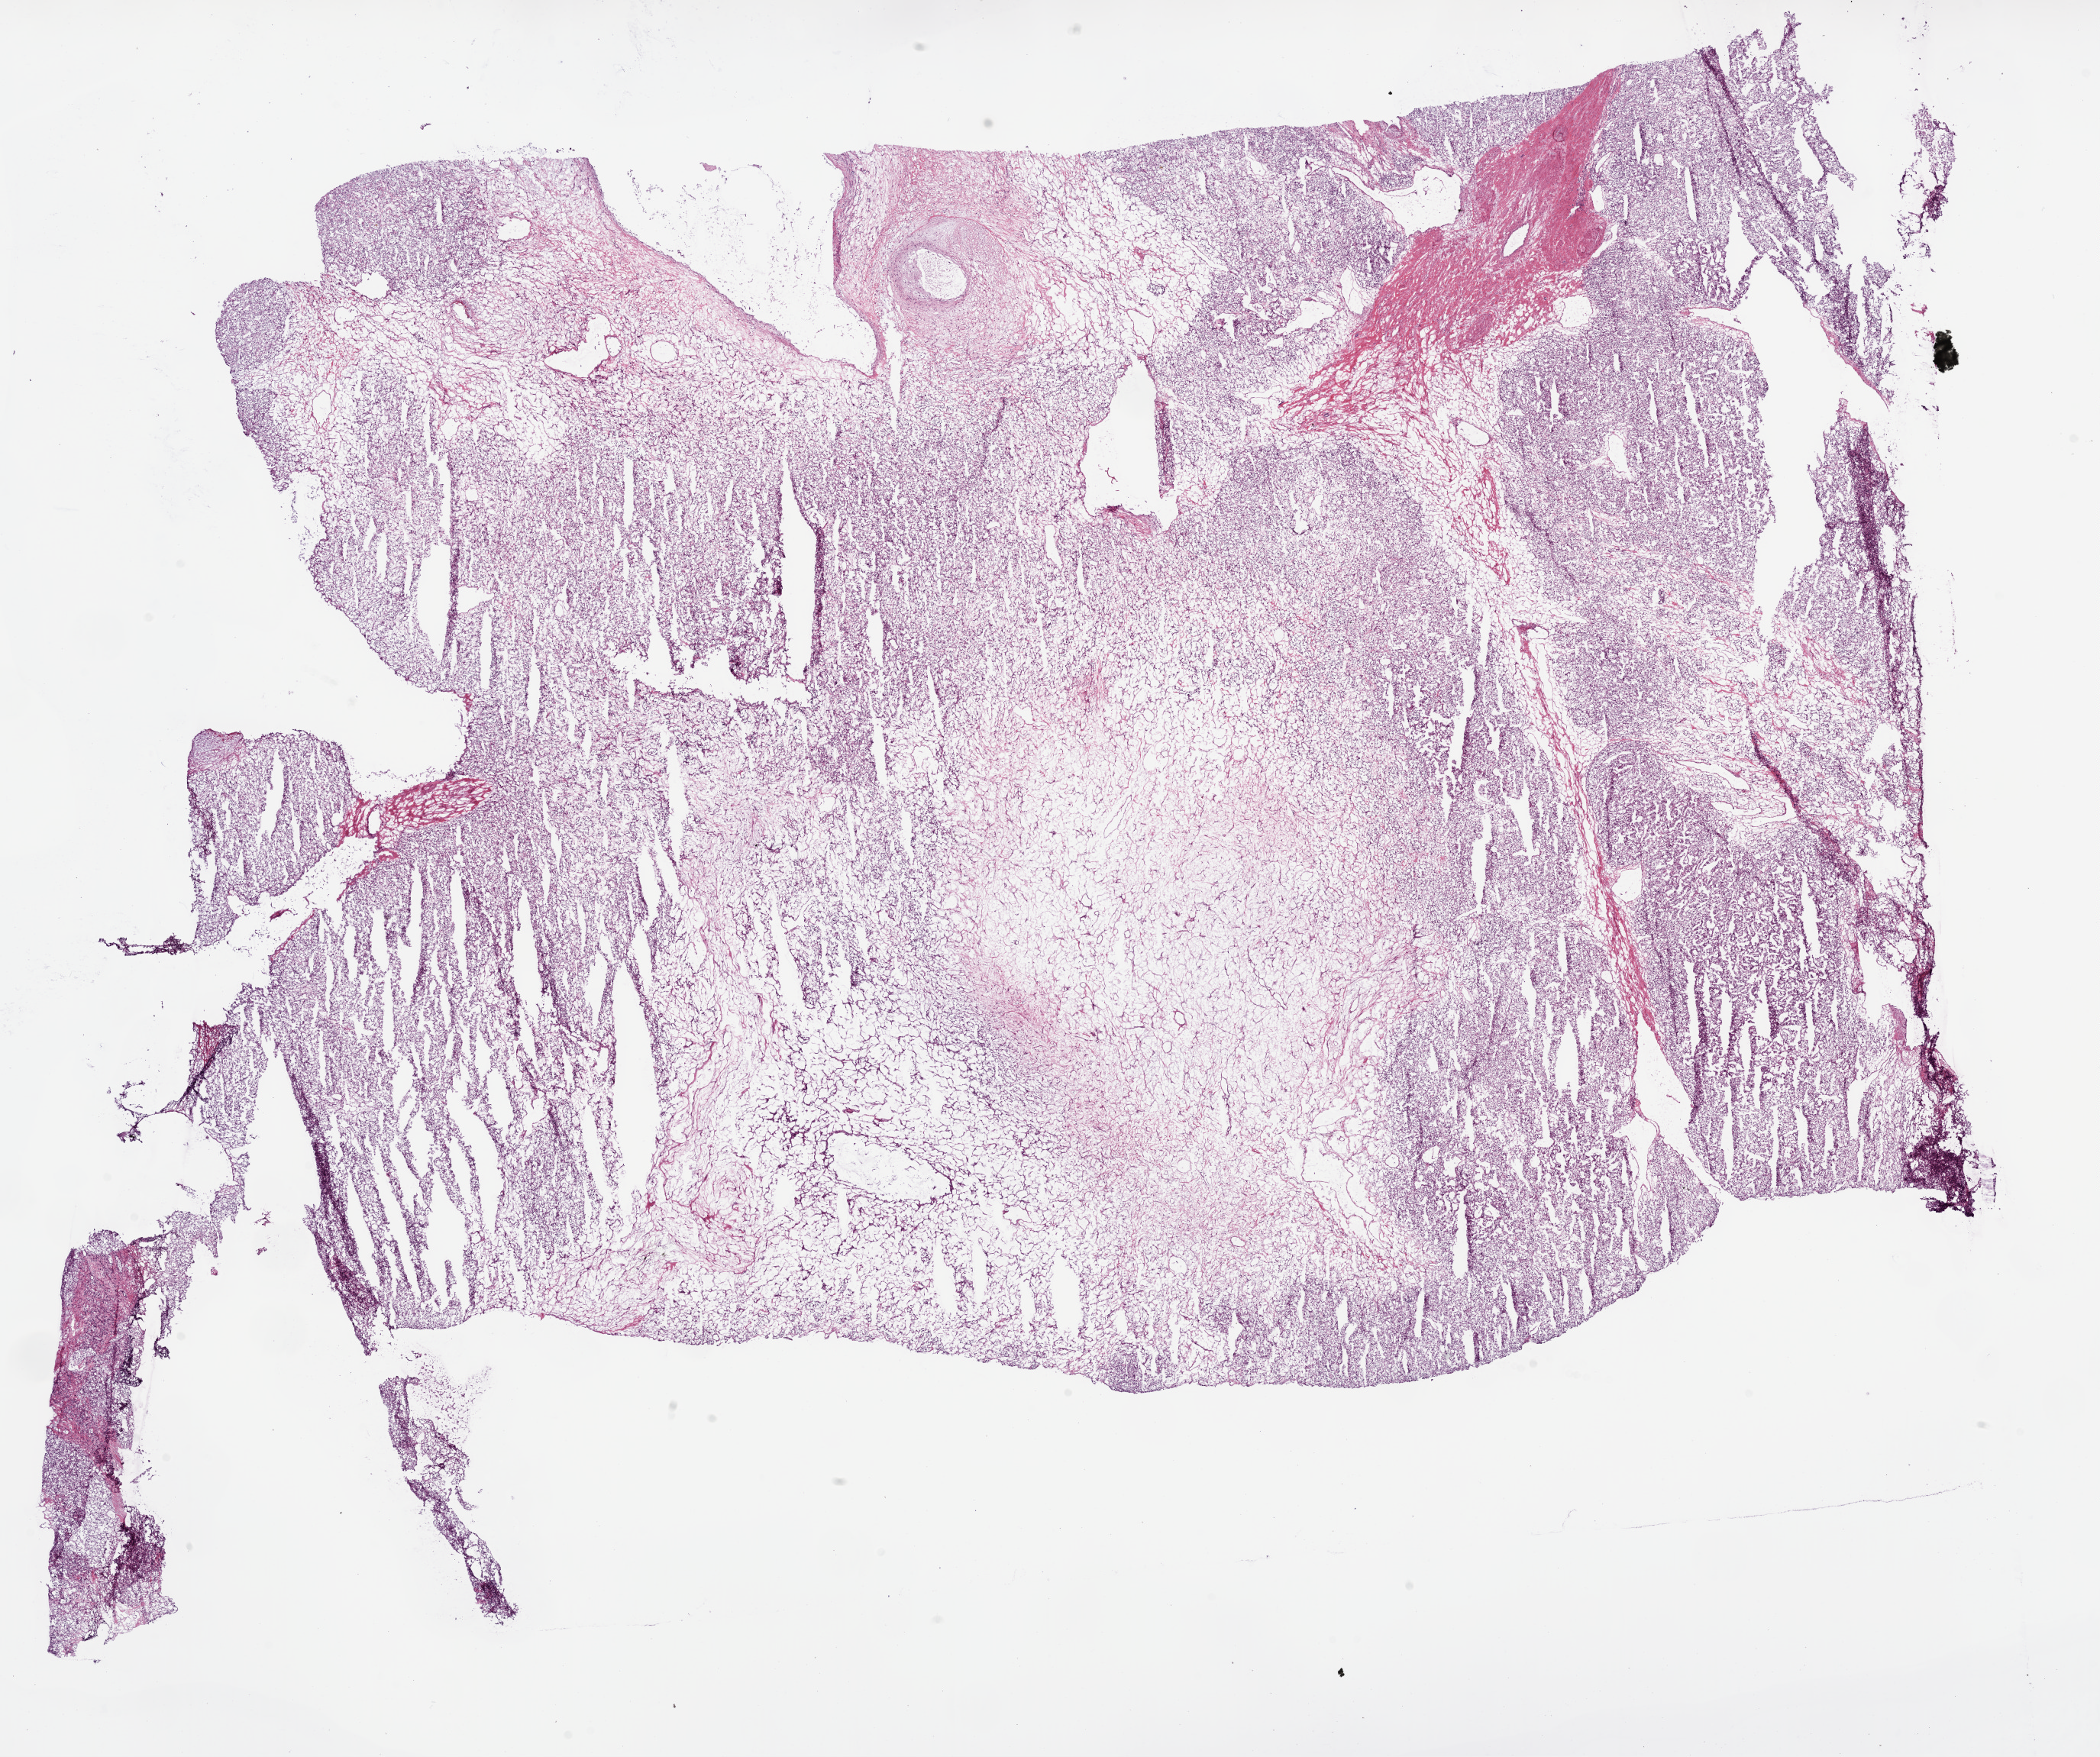
Digitized H&E-stained tissue section (whole slide), shown as a low-resolution overview of the whole scanned area (about 22.1 x 18.5 mm); frozen section; kidney, primary tumour sample. Patient: female, age at initial diagnosis 46 years. Histologic grade: G3 (poorly differentiated). Composition of this section per pathologist review: tumour cells 80%, tumour nuclei 80%, normal cells 0%, stromal cells 20%, necrosis 0%.
- diagnosis: Clear cell adenocarcinoma, NOS
- TNM: T1a NX M0
- AJCC pathologic stage: I
- laterality: right